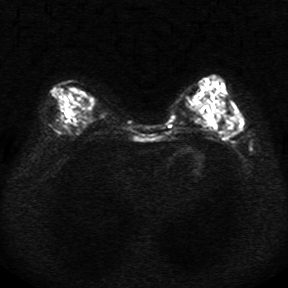
Breast MRI, one axial slice; position 13 of 34 along the scan axis; diffusion-weighted series; image 2 of 4 stored at this slice position (different b-values; order by instance number); 1.5 T; 5 mm slice thickness; 288 × 288 image matrix. Female patient.
Annotated regions visible in this slice (outlined manually by an expert reader):
- tumour on diffusion-weighted imaging: box from (x=236, y=118) to (x=241, y=132) px